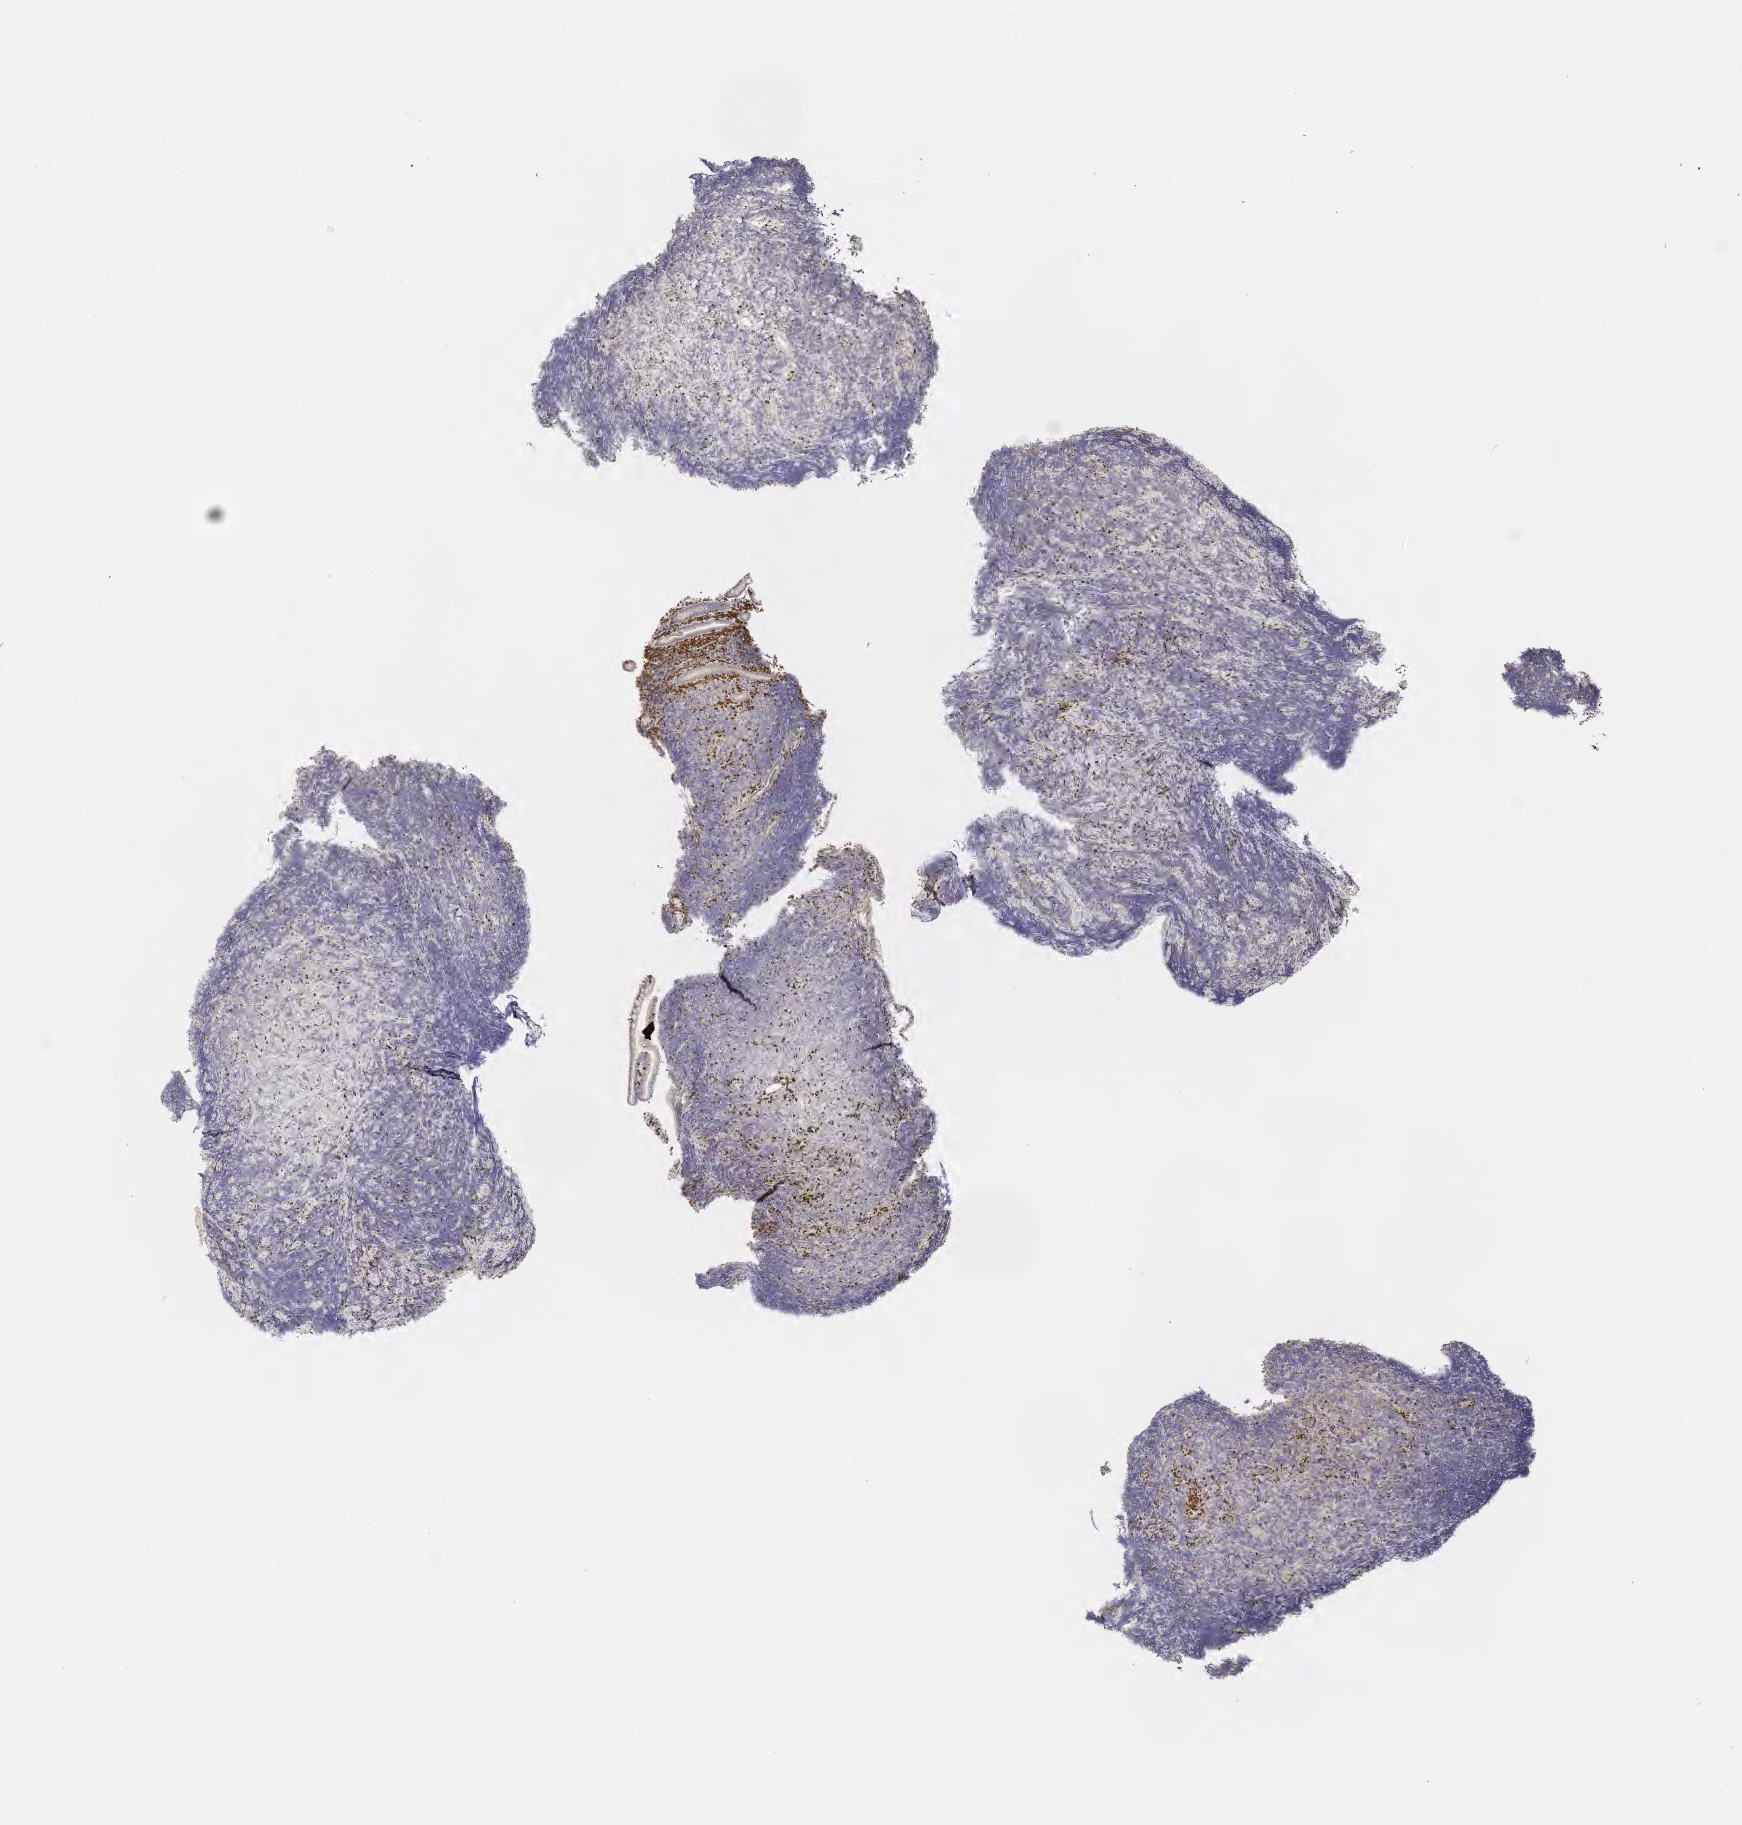
IHC for CD3, whole-slide image — low-resolution overview of the scanned area, about 7.0 x 7.4 mm; tumor tissue; anatomic site: small intestine. Female patient, age 47 years.
Diagnosis: Burkitt lymphoma, NOS.